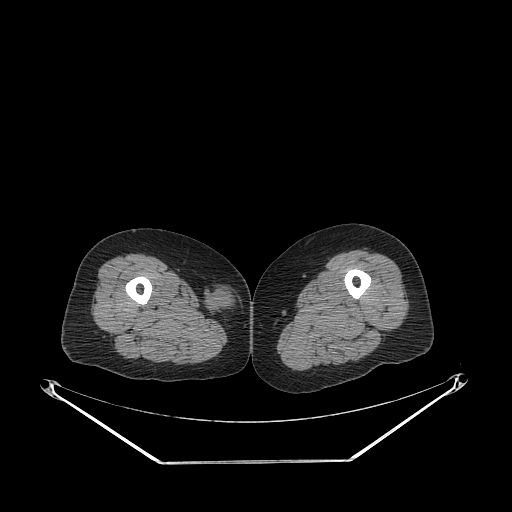
CT of an extremity soft-tissue mass (from a PET/CT study), one axial slice. Position 228 of 311 along the scan axis. 140 kVp. Soft-tissue window (W 400 / L 40 HU). 512 × 512 image matrix, field of view 500 × 500 mm. Female patient. Case-level facts recorded for this patient, not image findings: histological type: leiomyosarcoma; grade: intermediate; site of the primary tumour: parascapusular.
Structures marked on this image (expert contour drawn on MRI and transferred to this co-registered scan by the dataset authors):
- gross tumour volume including surrounding oedema: bounding box (x1, y1, x2, y2) in pixels: (206, 290, 236, 314)
- gross tumour volume (mass): (208, 292, 234, 312)